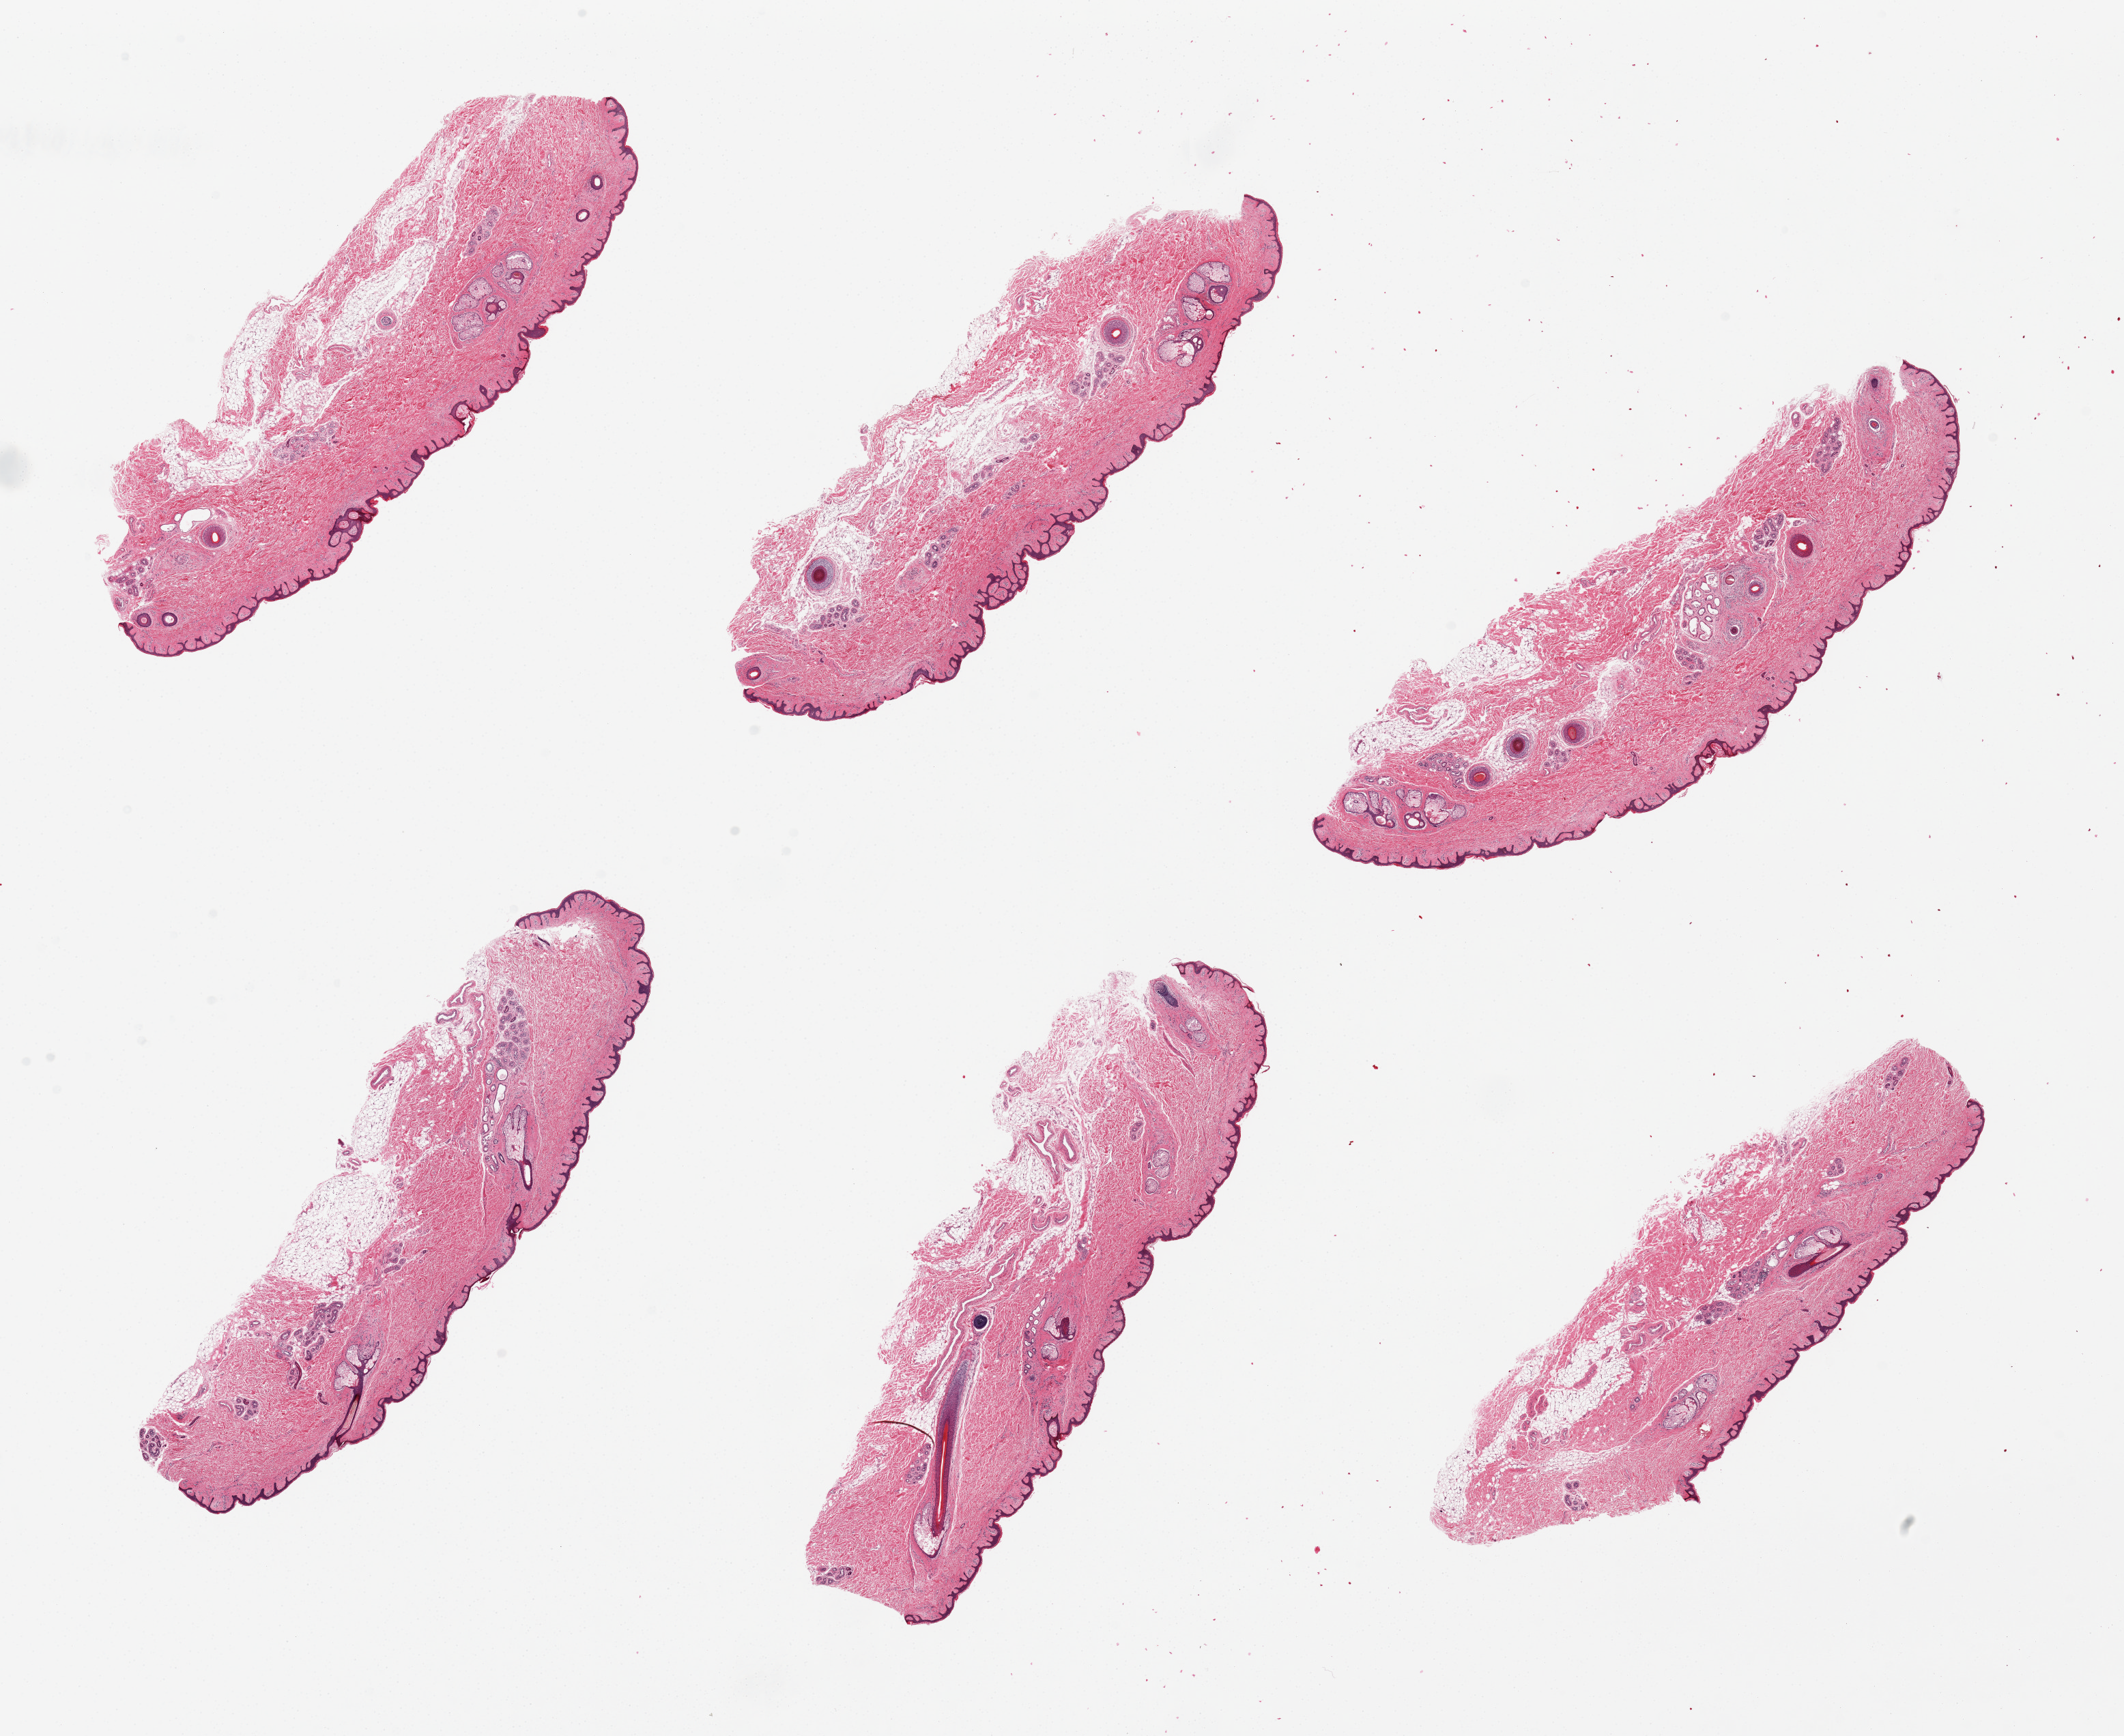
Hematoxylin and eosin (H&E) whole-slide image, brightfield, low-resolution overview of the scanned area, about 24.6 x 20.1 mm. PAXgene-fixed paraffin-embedded (PFPE) section. Section of skin of suprapubic region (target tissue). Donor tissue sample.
Review note (as recorded): 6 pieces; minimal residual adipose tissue.